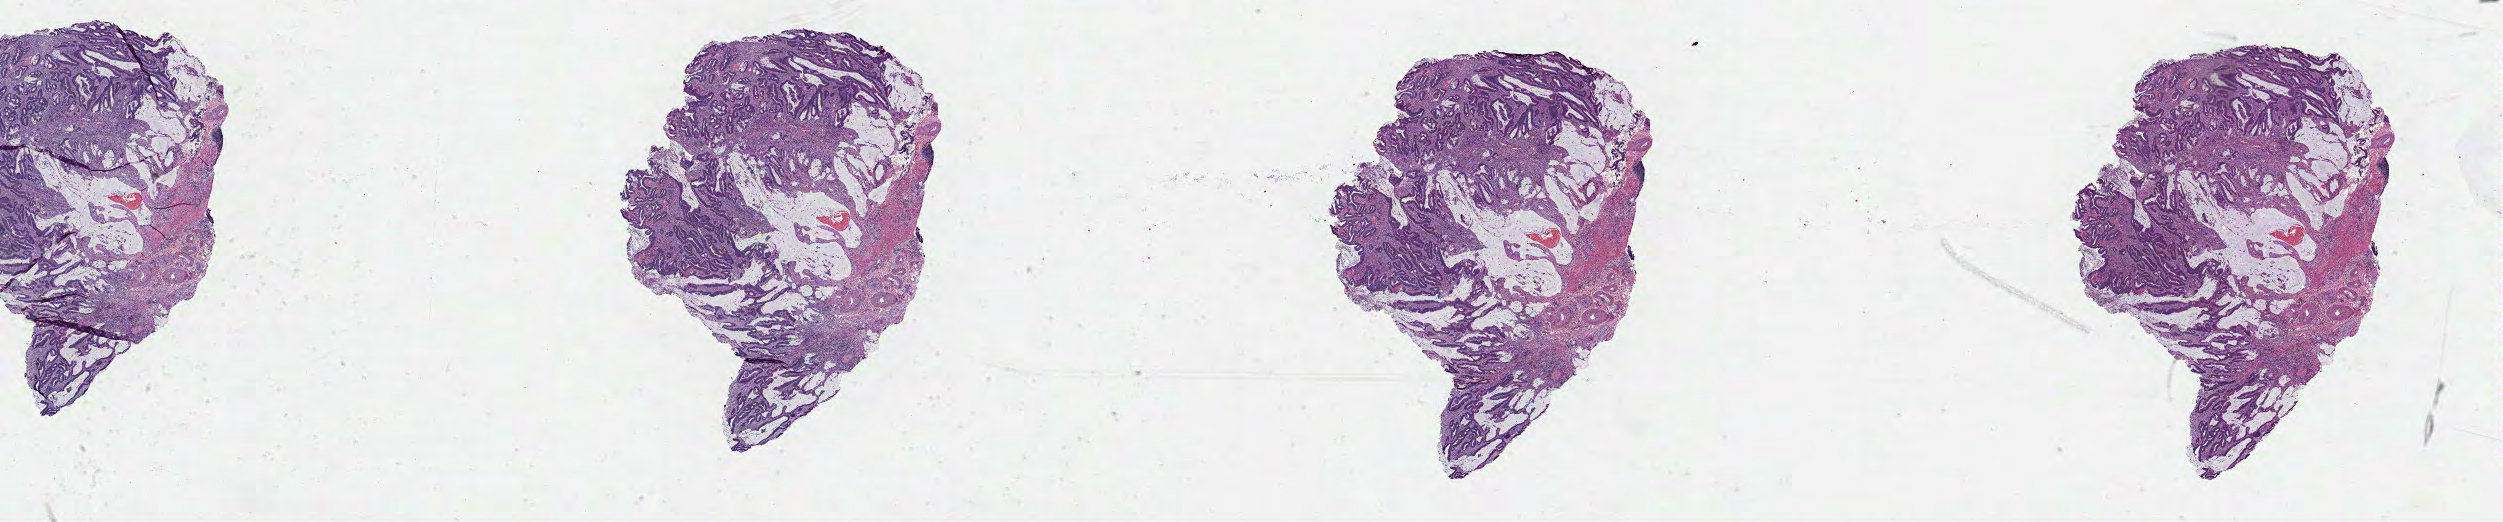
H&E-stained whole-slide image — low-resolution overview of the scanned area, about 40.4 x 8.4 mm (slide scanned at 40x). Formalin-fixed paraffin-embedded (FFPE) diagnostic section. Colon, primary tumour sample. Male, age 82 years at initial diagnosis.
Lymph nodes positive (case pathology): 0 of 12 examined. AJCC pathologic stage: I (7th edition). Diagnosis: Adenocarcinoma, NOS. TNM: T2 N0 M0.